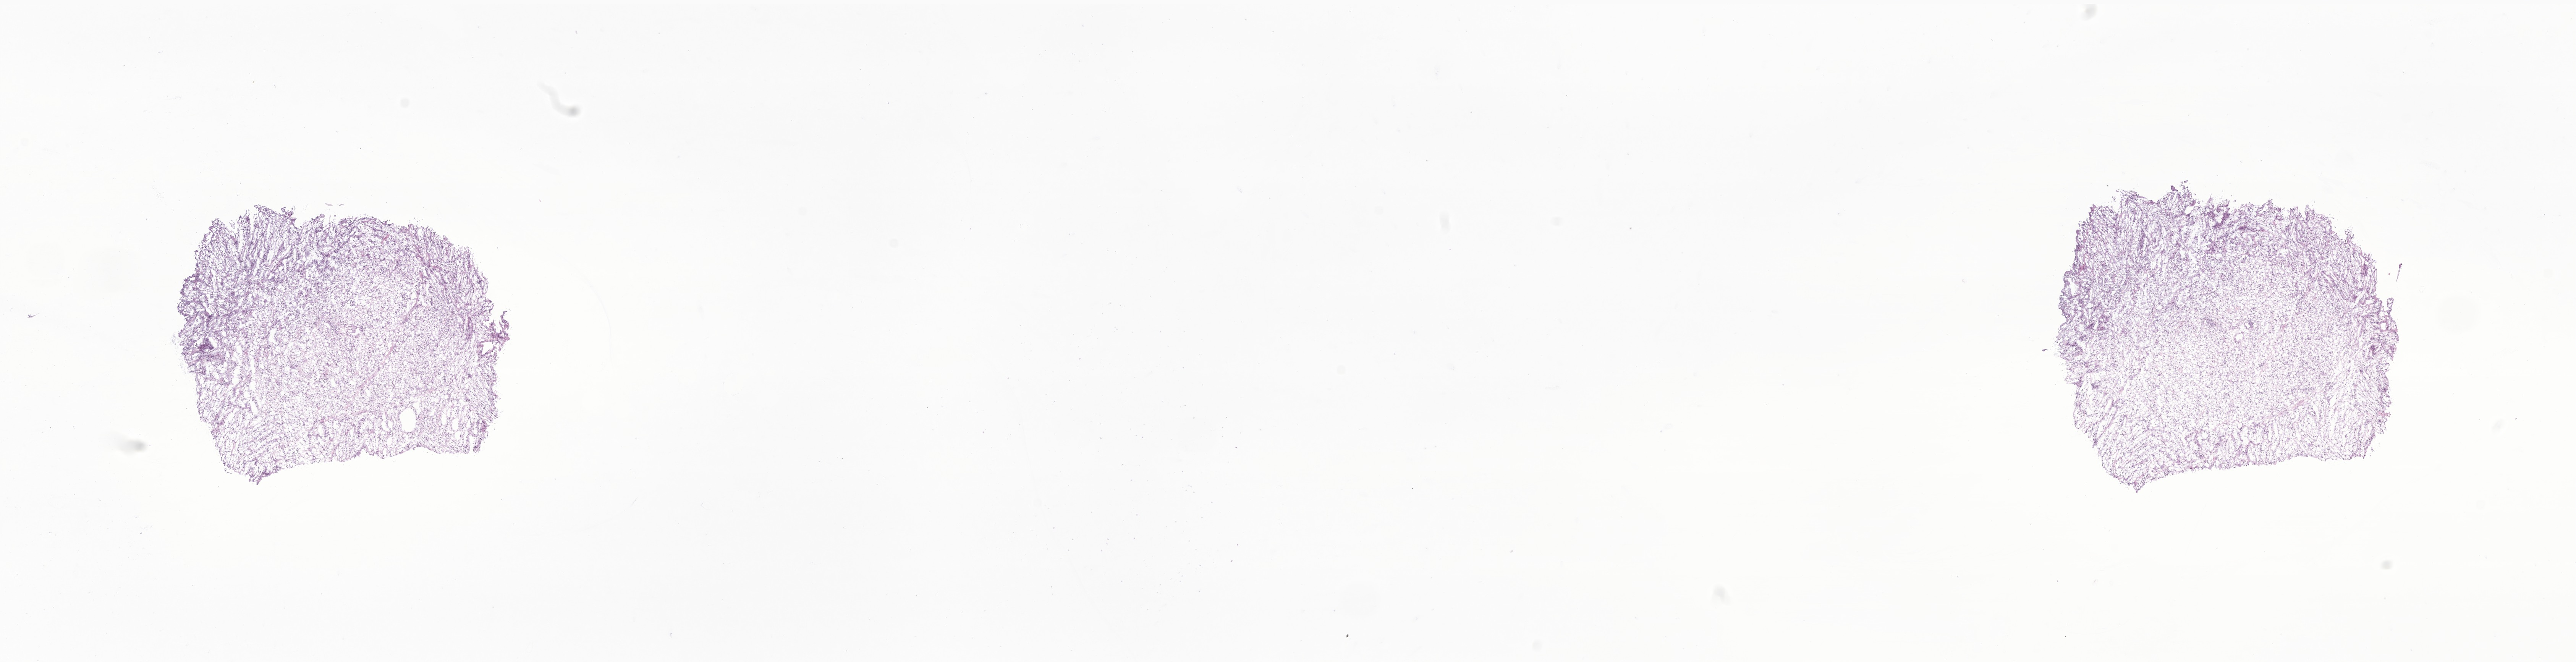
Hematoxylin and eosin (H&E) whole-slide image of tumor tissue from the testis — whole scanned area (about 28.4 x 7.3 mm) shown as a low-resolution overview, frozen section. Male patient, age 144 months (12 years).
• diagnosis: Rhabdomyosarcoma, NOS